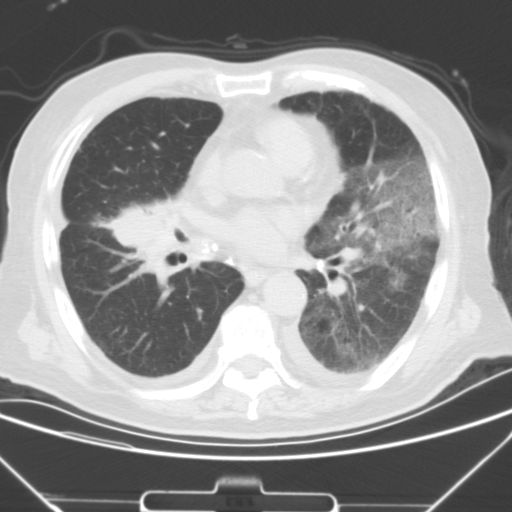
Chest CT, one axial slice. Slice 16 of 43 in the series (ordered by position). 120 kVp. Lung window (W 1500 / L -600 HU). 5 mm slice thickness. 512 × 512 image matrix. Patient: male, 85 years. From the clinical record (not read from this slice): clinical TNM (as recorded): T4 N3 M2.
Structures marked on this image (rectangle marked by the reading radiologist):
- lung tumour (recorded histology: squamous cell carcinoma): box from (x=97, y=194) to (x=184, y=288) px